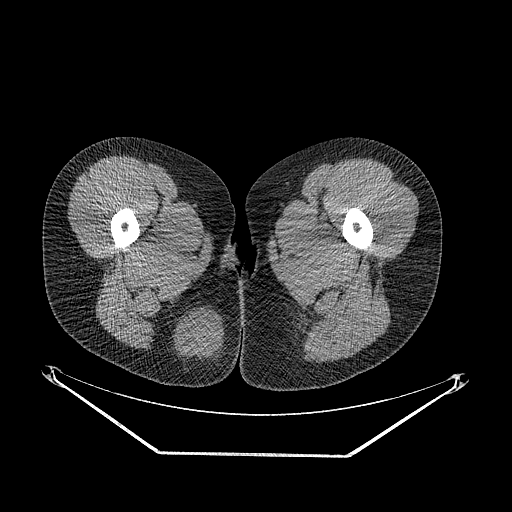
CT of an extremity soft-tissue mass (from a PET/CT study), one axial slice. Slice 22 of 267 in the series (ordered by position). Soft-tissue window (W 400 / L 40 HU). 3.75 mm slice thickness. 512 × 512 image matrix, field of view 500 × 500 mm. Female patient. Case-level facts recorded for this patient, not image findings: histological type: epithelioid sarcoma; grade: intermediate; site of the primary tumour: right buttock.
Outlined on this slice (expert contour drawn on MRI and transferred to this co-registered scan by the dataset authors):
- gross tumour volume including surrounding oedema: bounding box <171,306,229,378> (left, top, right, bottom; pixels)
- gross tumour volume (mass): <176,311,223,359>